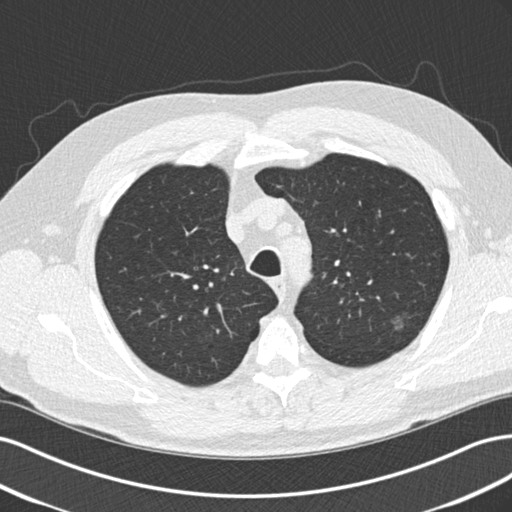
Low-dose screening chest CT, one axial slice. Slice 166 of 209 in the series (ordered by position). Lung window (W 1500 / L -600 HU). 2 mm slice thickness. 512 × 512 image matrix, field of view 360 × 360 mm.
Structures marked on this image (manually delineated by an expert):
- lesion 1 (tumor, upper lobe of left lung): bounding box (x1, y1, x2, y2) in pixels: (394, 317, 403, 330)